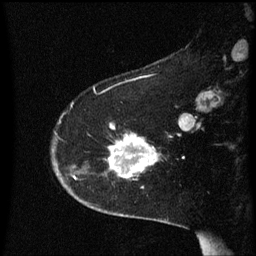
Breast MRI (dynamic contrast-enhanced), one sagittal slice; position 43 of 60 along the scan axis; dynamic contrast-enhanced series, image 2 of 3 at this slice position (ordered by acquisition); 1.5 T; TE 4.2 ms, TR 8.4 ms; 256 × 256 image matrix. Patient: female, 54 years. From the clinical record (not read from this slice): setting: breast cancer imaged before/during neoadjuvant chemotherapy; receptor status: HR-positive, HER2-negative.
Structures marked on this image (semi-automatically segmented with operator editing):
- analysis volume of interest (the breast-tissue region the enhancement analysis was run in; not a lesion): box from (x=106, y=124) to (x=162, y=189) px
- tumour enhancement mask (voxels above the 70 % enhancement threshold inside the analysis volume of interest): (x=110, y=126)–(x=159, y=179)